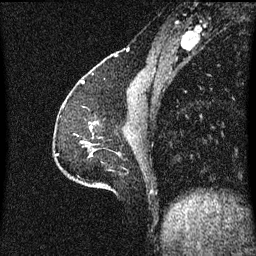
Breast MRI (dynamic contrast-enhanced), one sagittal slice. Slice 20 of 60 in the series (ordered by position). Dynamic contrast-enhanced series, image 2 of 3 at this slice position (ordered by acquisition). 1.5 T. TE 4.2 ms, TR 8.4 ms. 2 mm slice thickness. 256 × 256 image matrix, field of view 200 × 200 mm. Patient: female, 51 years.
Structures marked on this image (semi-automatically segmented with operator editing):
- analysis volume of interest (the breast-tissue region the enhancement analysis was run in; not a lesion): bounding box (x1, y1, x2, y2) in pixels: (89, 122, 102, 139)
- tumour enhancement mask (voxels above the 70 % enhancement threshold inside the analysis volume of interest): (90, 122, 98, 129)